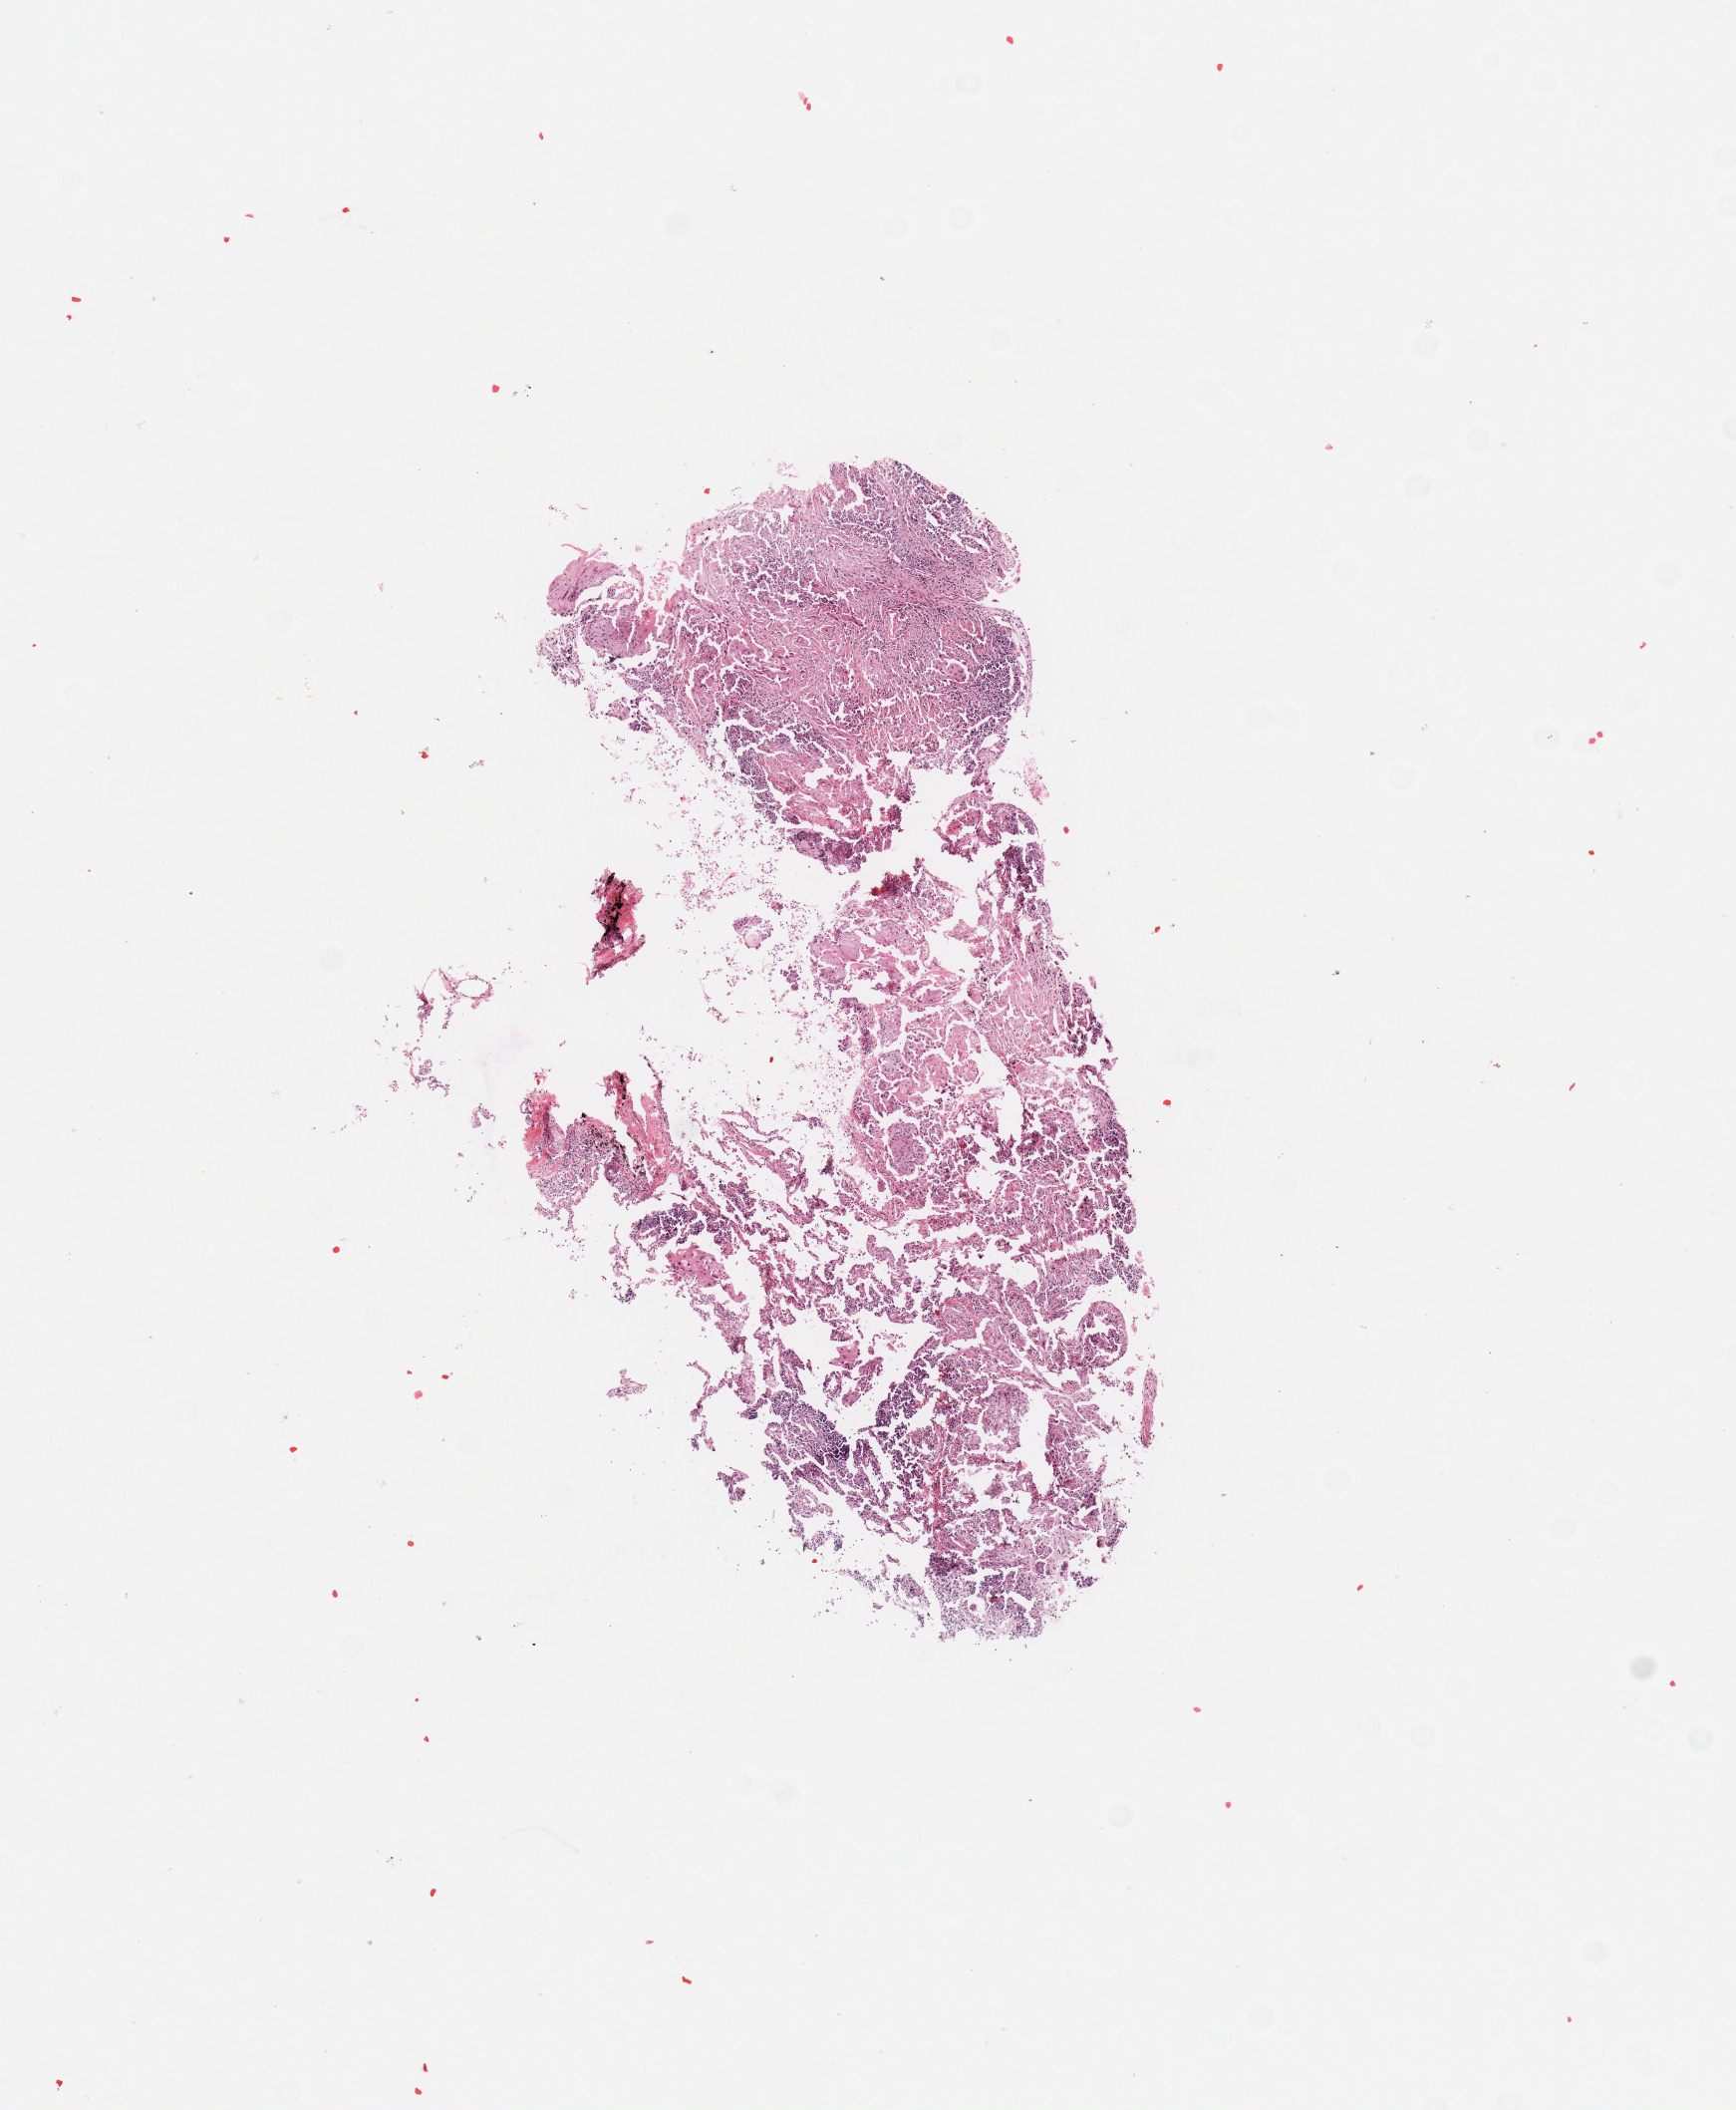
Whole-slide histology image, Hematoxylin and eosin (H&E) stained, whole scanned area (about 6.9 x 8.4 mm, slide scanned at 20x) shown as a low-resolution overview; tumour tissue sample, sampled site: lung. 56-year-old female patient. Histologic grade: G3 (poorly differentiated). Pathologist review of this section (percent, as recorded): tumour nuclei 70%, necrosis 5%.
AJCC pathologic stage: IIIA. Primary tumour site (as recorded): left lower lobe. Diagnosis: Squamous cell carcinoma, NOS.